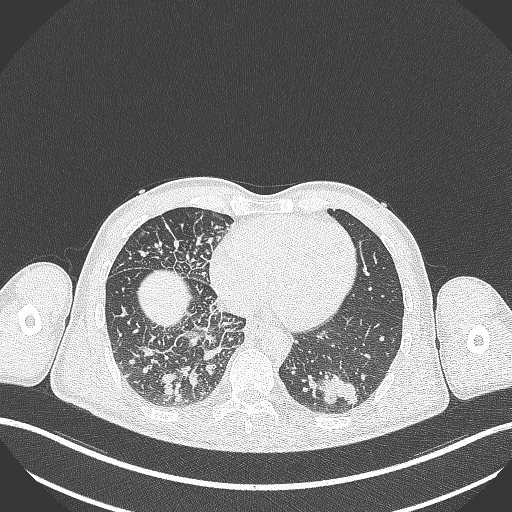
Chest CT, one axial slice. Lung window (W 1500 / L -600 HU). 1 mm slice thickness. 512 × 512 image matrix, field of view 400 × 400 mm. Male patient, age 49 years. From the clinical record (not read from this slice): clinical TNM (as recorded): T2b N1 M0.
Structures marked on this image (rectangle marked by the reading radiologist):
- lung tumour (recorded histology: adenocarcinoma): bounding box <315,368,364,407> (left, top, right, bottom; pixels)